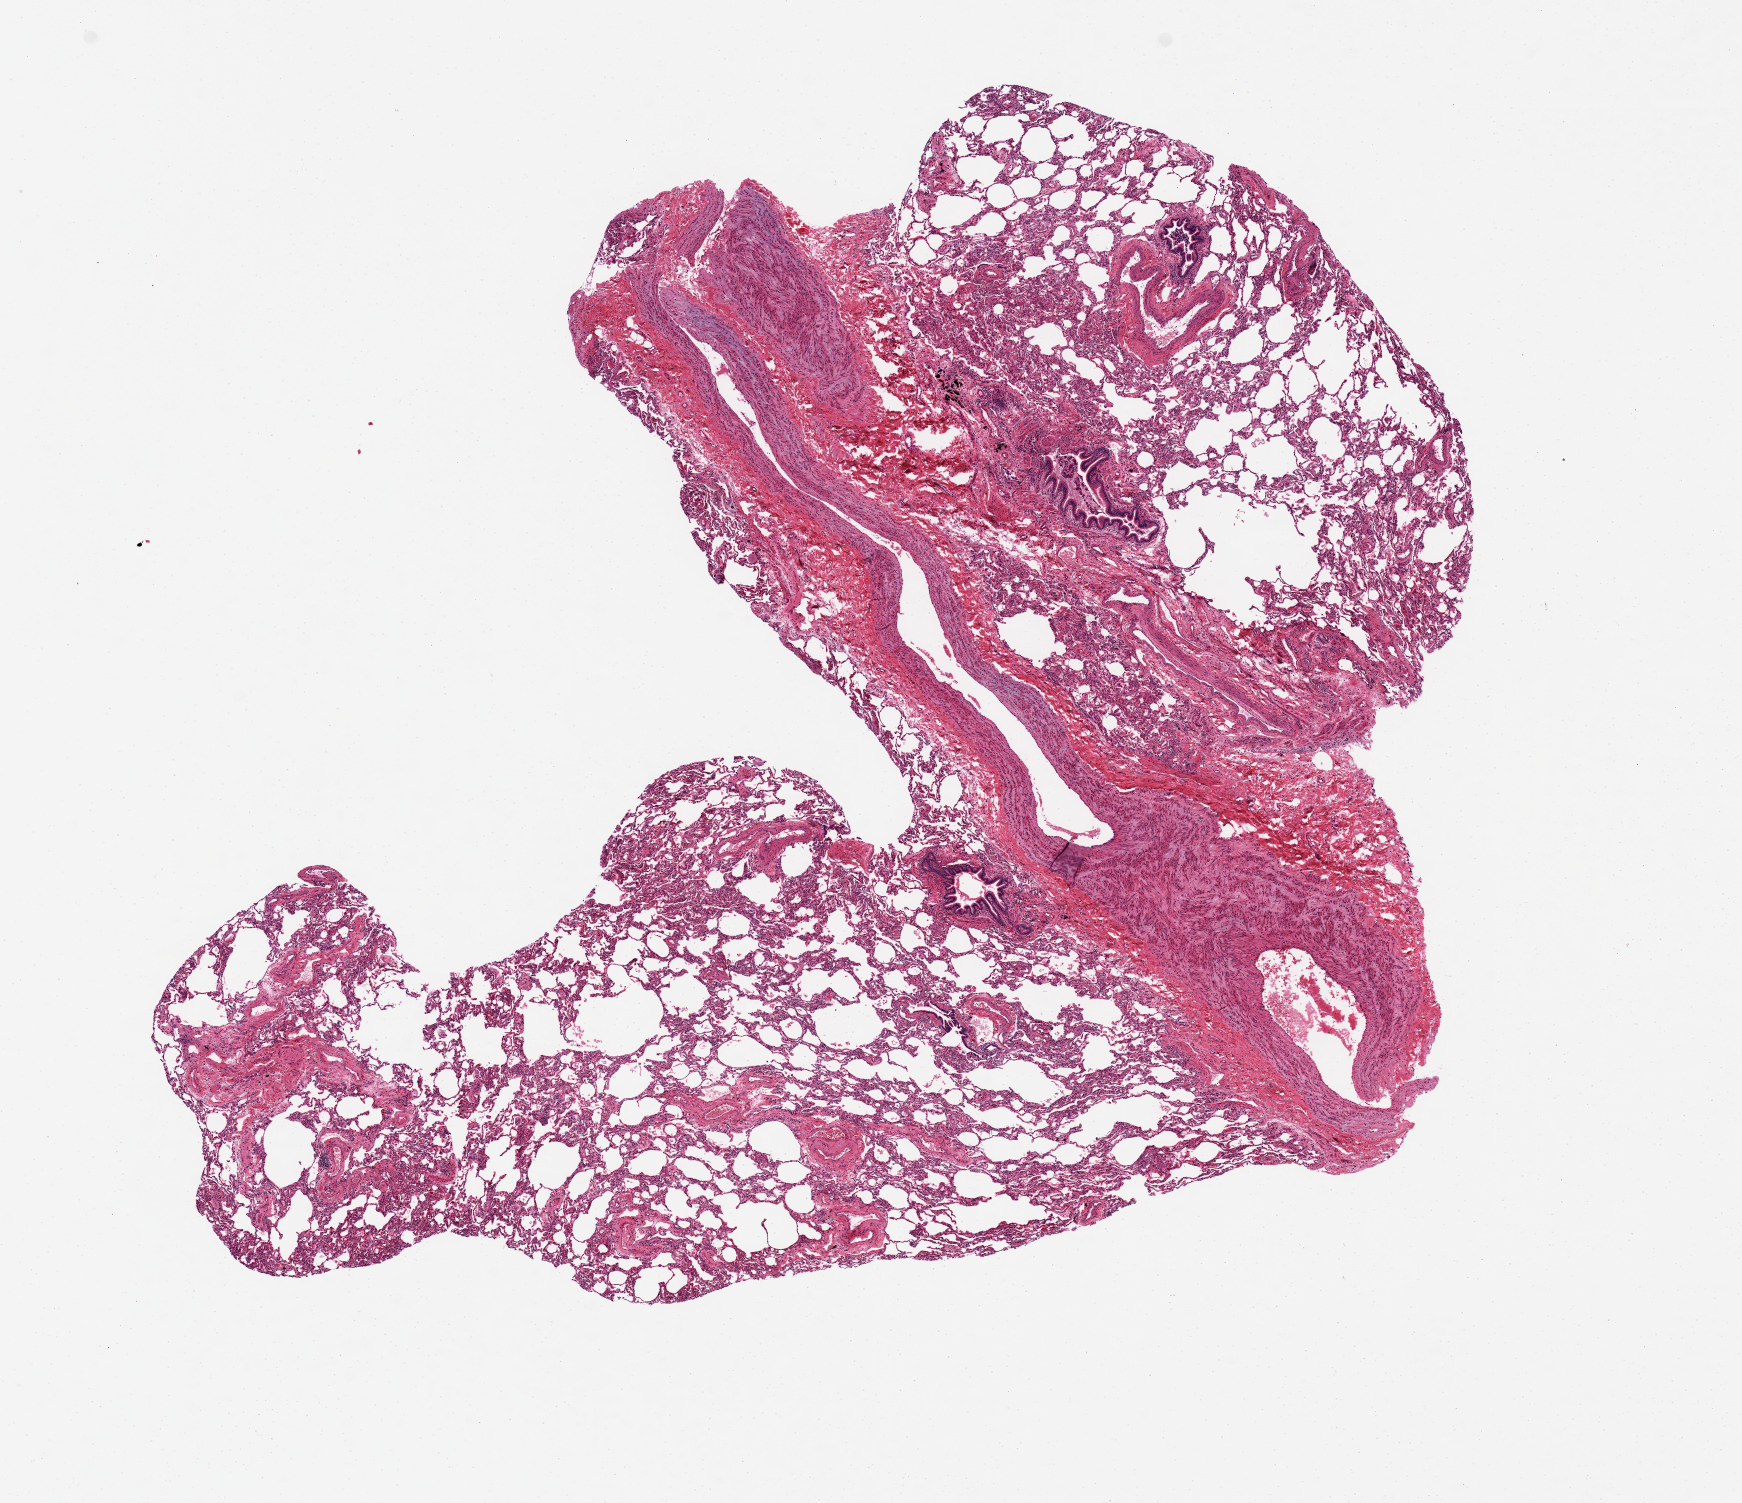
Hematoxylin and eosin (H&E) whole-slide image — shown as a low-resolution overview of the whole scanned area (about 13.8 x 11.9 mm). PAXgene-fixed paraffin-embedded (PFPE) section. Sampled site (target tissue): lung. Tissue donor sample. Donor sex: male.
Pathologist's review note for this sample: Mild emphysematous changes. 11.7 x 9.4 mm.